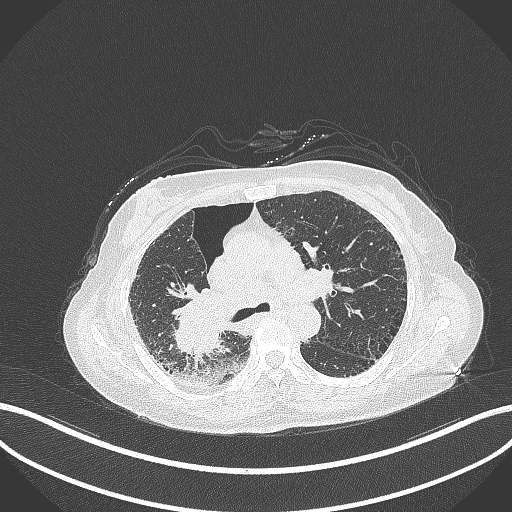
Chest CT, one axial slice. Position 221 of 408 along the scan axis. 120 kVp. Lung window (W 1500 / L -600 HU). 1 mm slice thickness. 512 × 512 image matrix, field of view 400 × 400 mm. Patient: female, 64 years. From the clinical record (not read from this slice): clinical TNM (as recorded): T3 N3 M0.
Structures marked on this image (bounding box drawn by a radiologist):
- lung tumour (recorded histology: squamous cell carcinoma): bounding box [x1, y1, x2, y2] px = [165, 284, 234, 365]